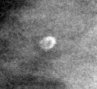
Region of interest cut from a scanned film mammogram (one marked finding); right breast; MLO view.
Finding: calcifications, morphology lucent center; BI-RADS assessment category 2; subtlety rating 3 on a 1 (subtle) to 5 (obvious) scale; benign; no additional work-up was recommended (benign without callback).